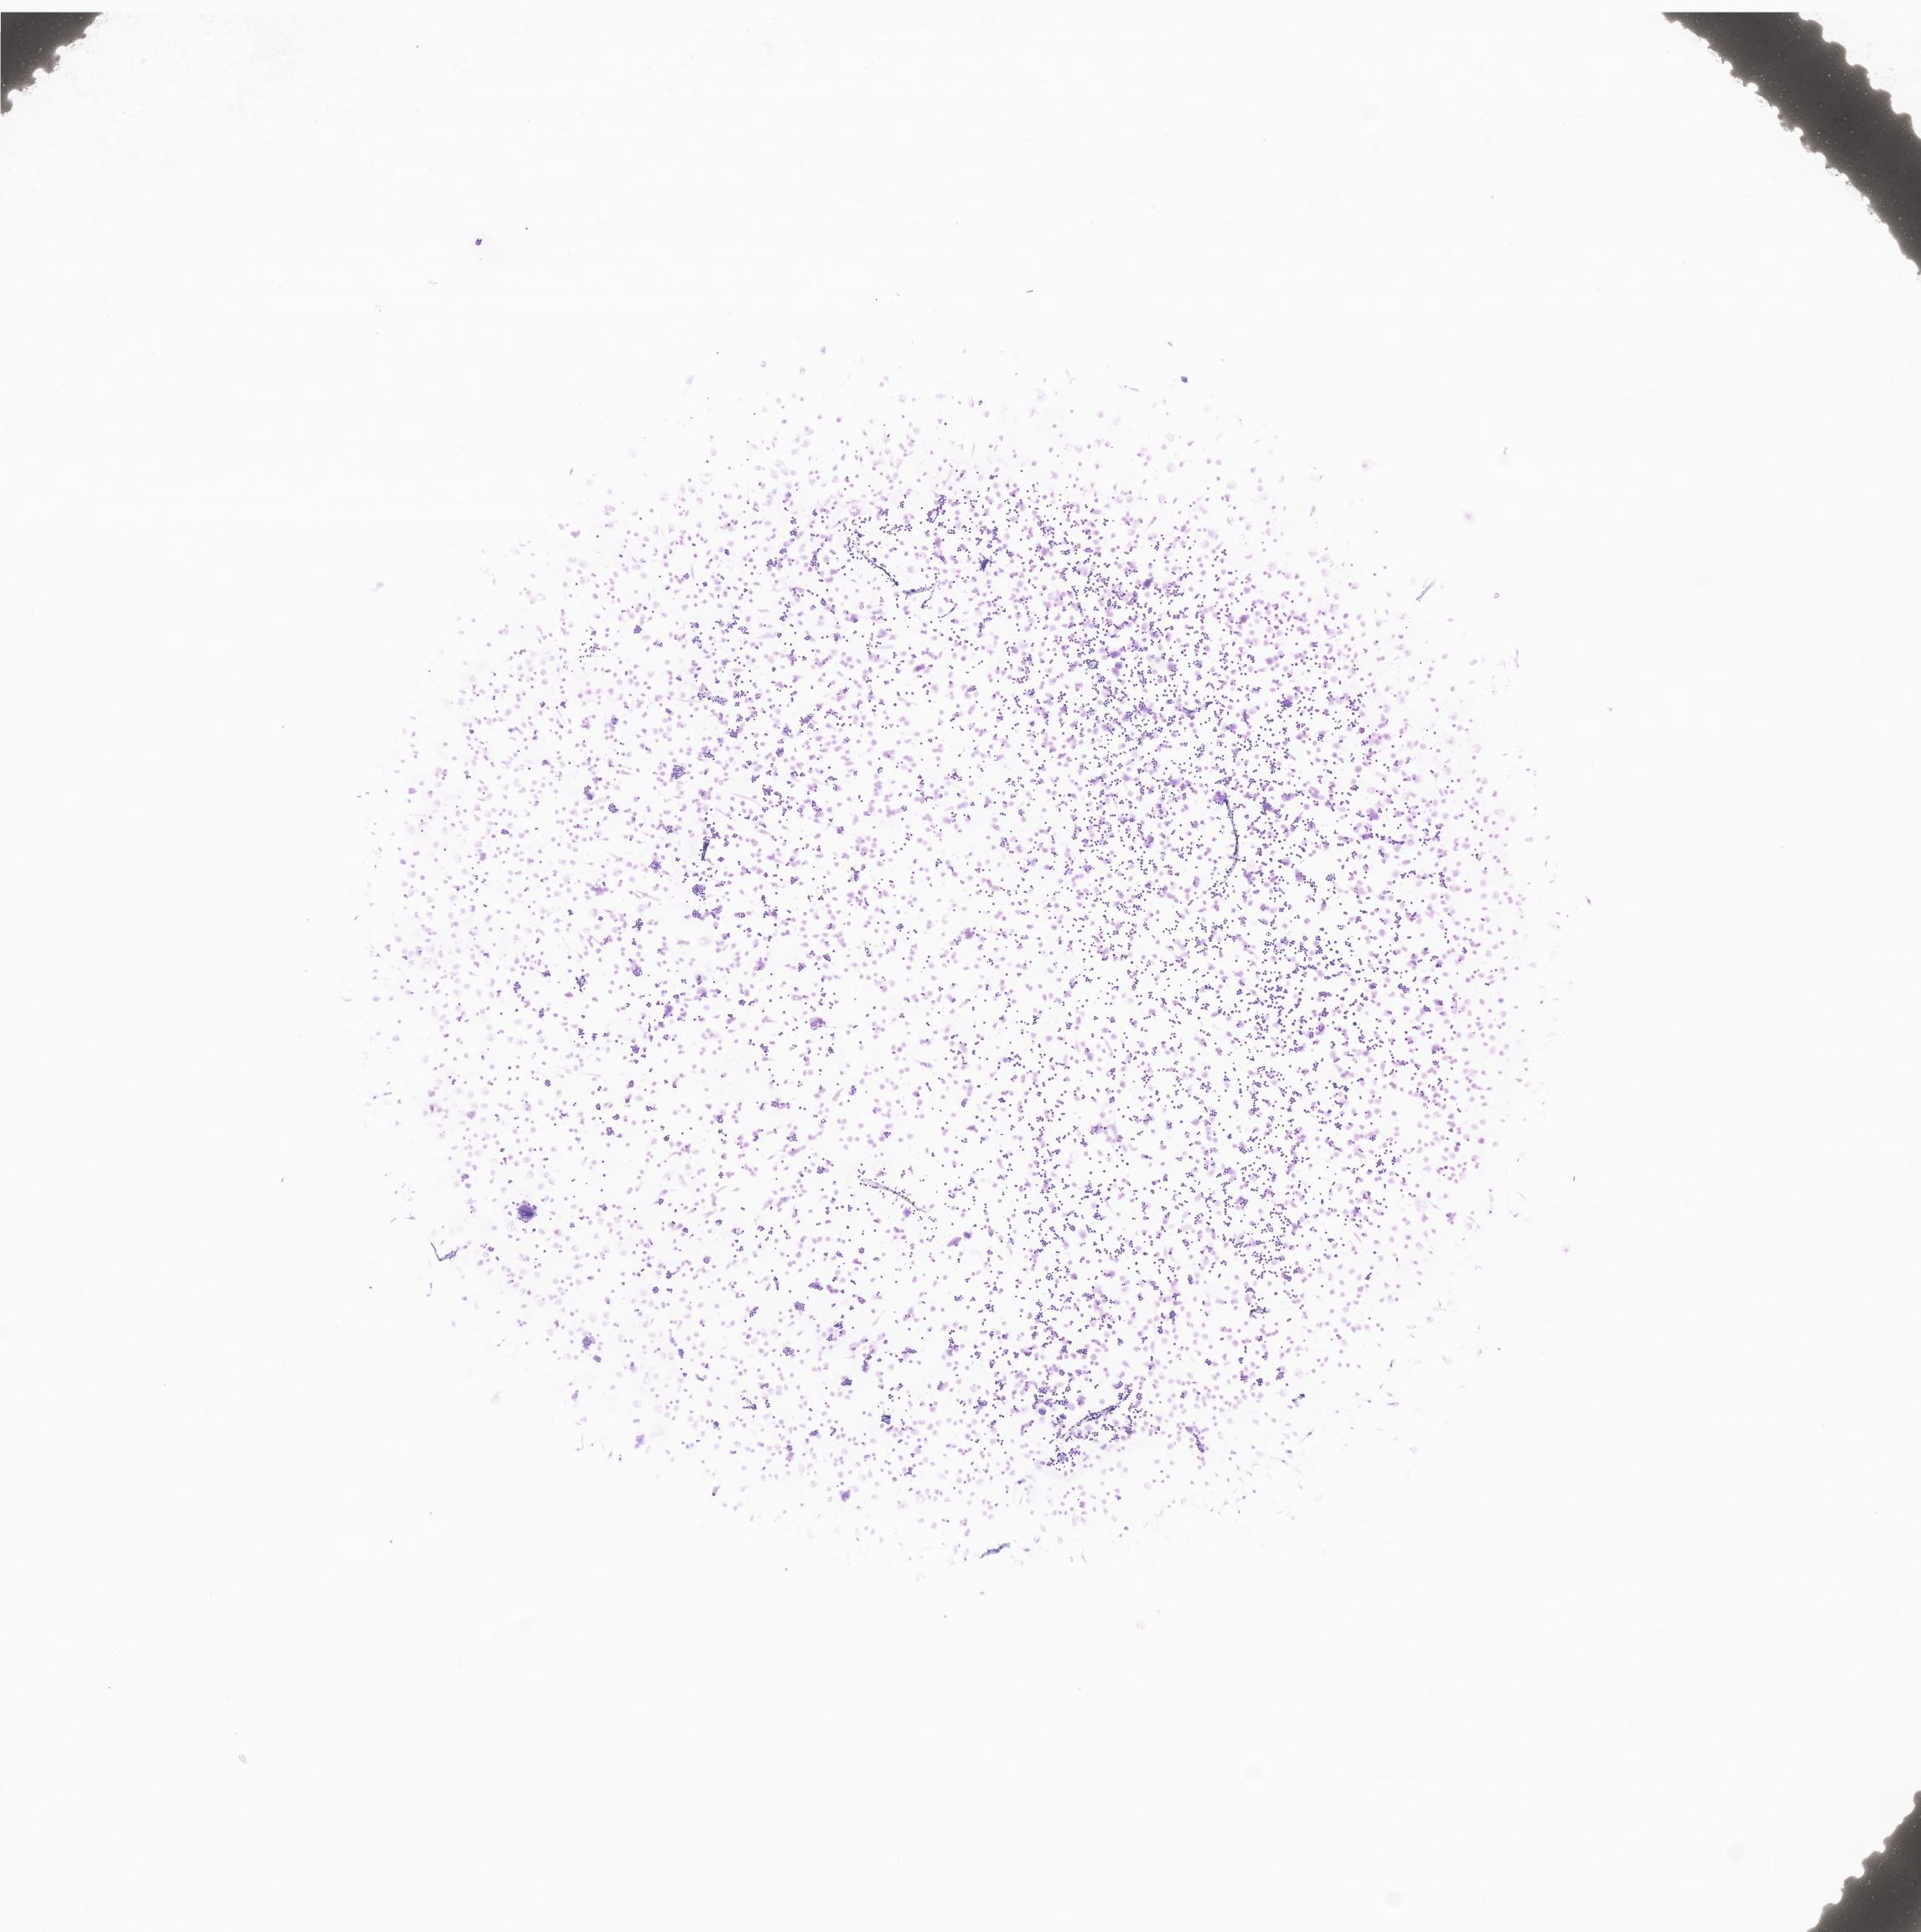
Whole-slide image of tumor tissue from the retroperitoneum — whole scanned area (about 9.7 x 9.7 mm) shown as a low-resolution overview. Female patient, age 65 months.
Diagnosis: Neuroblastoma, NOS.